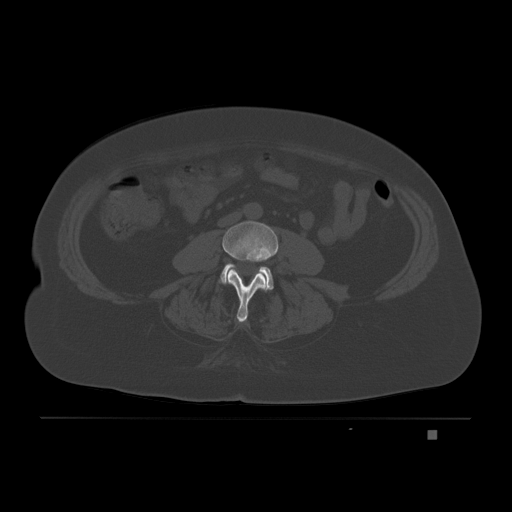
CT including the spine, one axial slice; slice 47 of 221 in the series (ordered by position); bone window (W 1800 / L 400 HU); 512 × 512 image matrix, field of view 474 × 474 mm. Patient: female, 63 years. From the clinical record (not read from this slice): primary cancer: breast.
Outlined on this slice (semi-automatically segmented with operator editing):
- L3 vertebra: bounding box (x1, y1, x2, y2) in pixels: (222, 221, 278, 322)
- L4 vertebra: (219, 263, 274, 291)